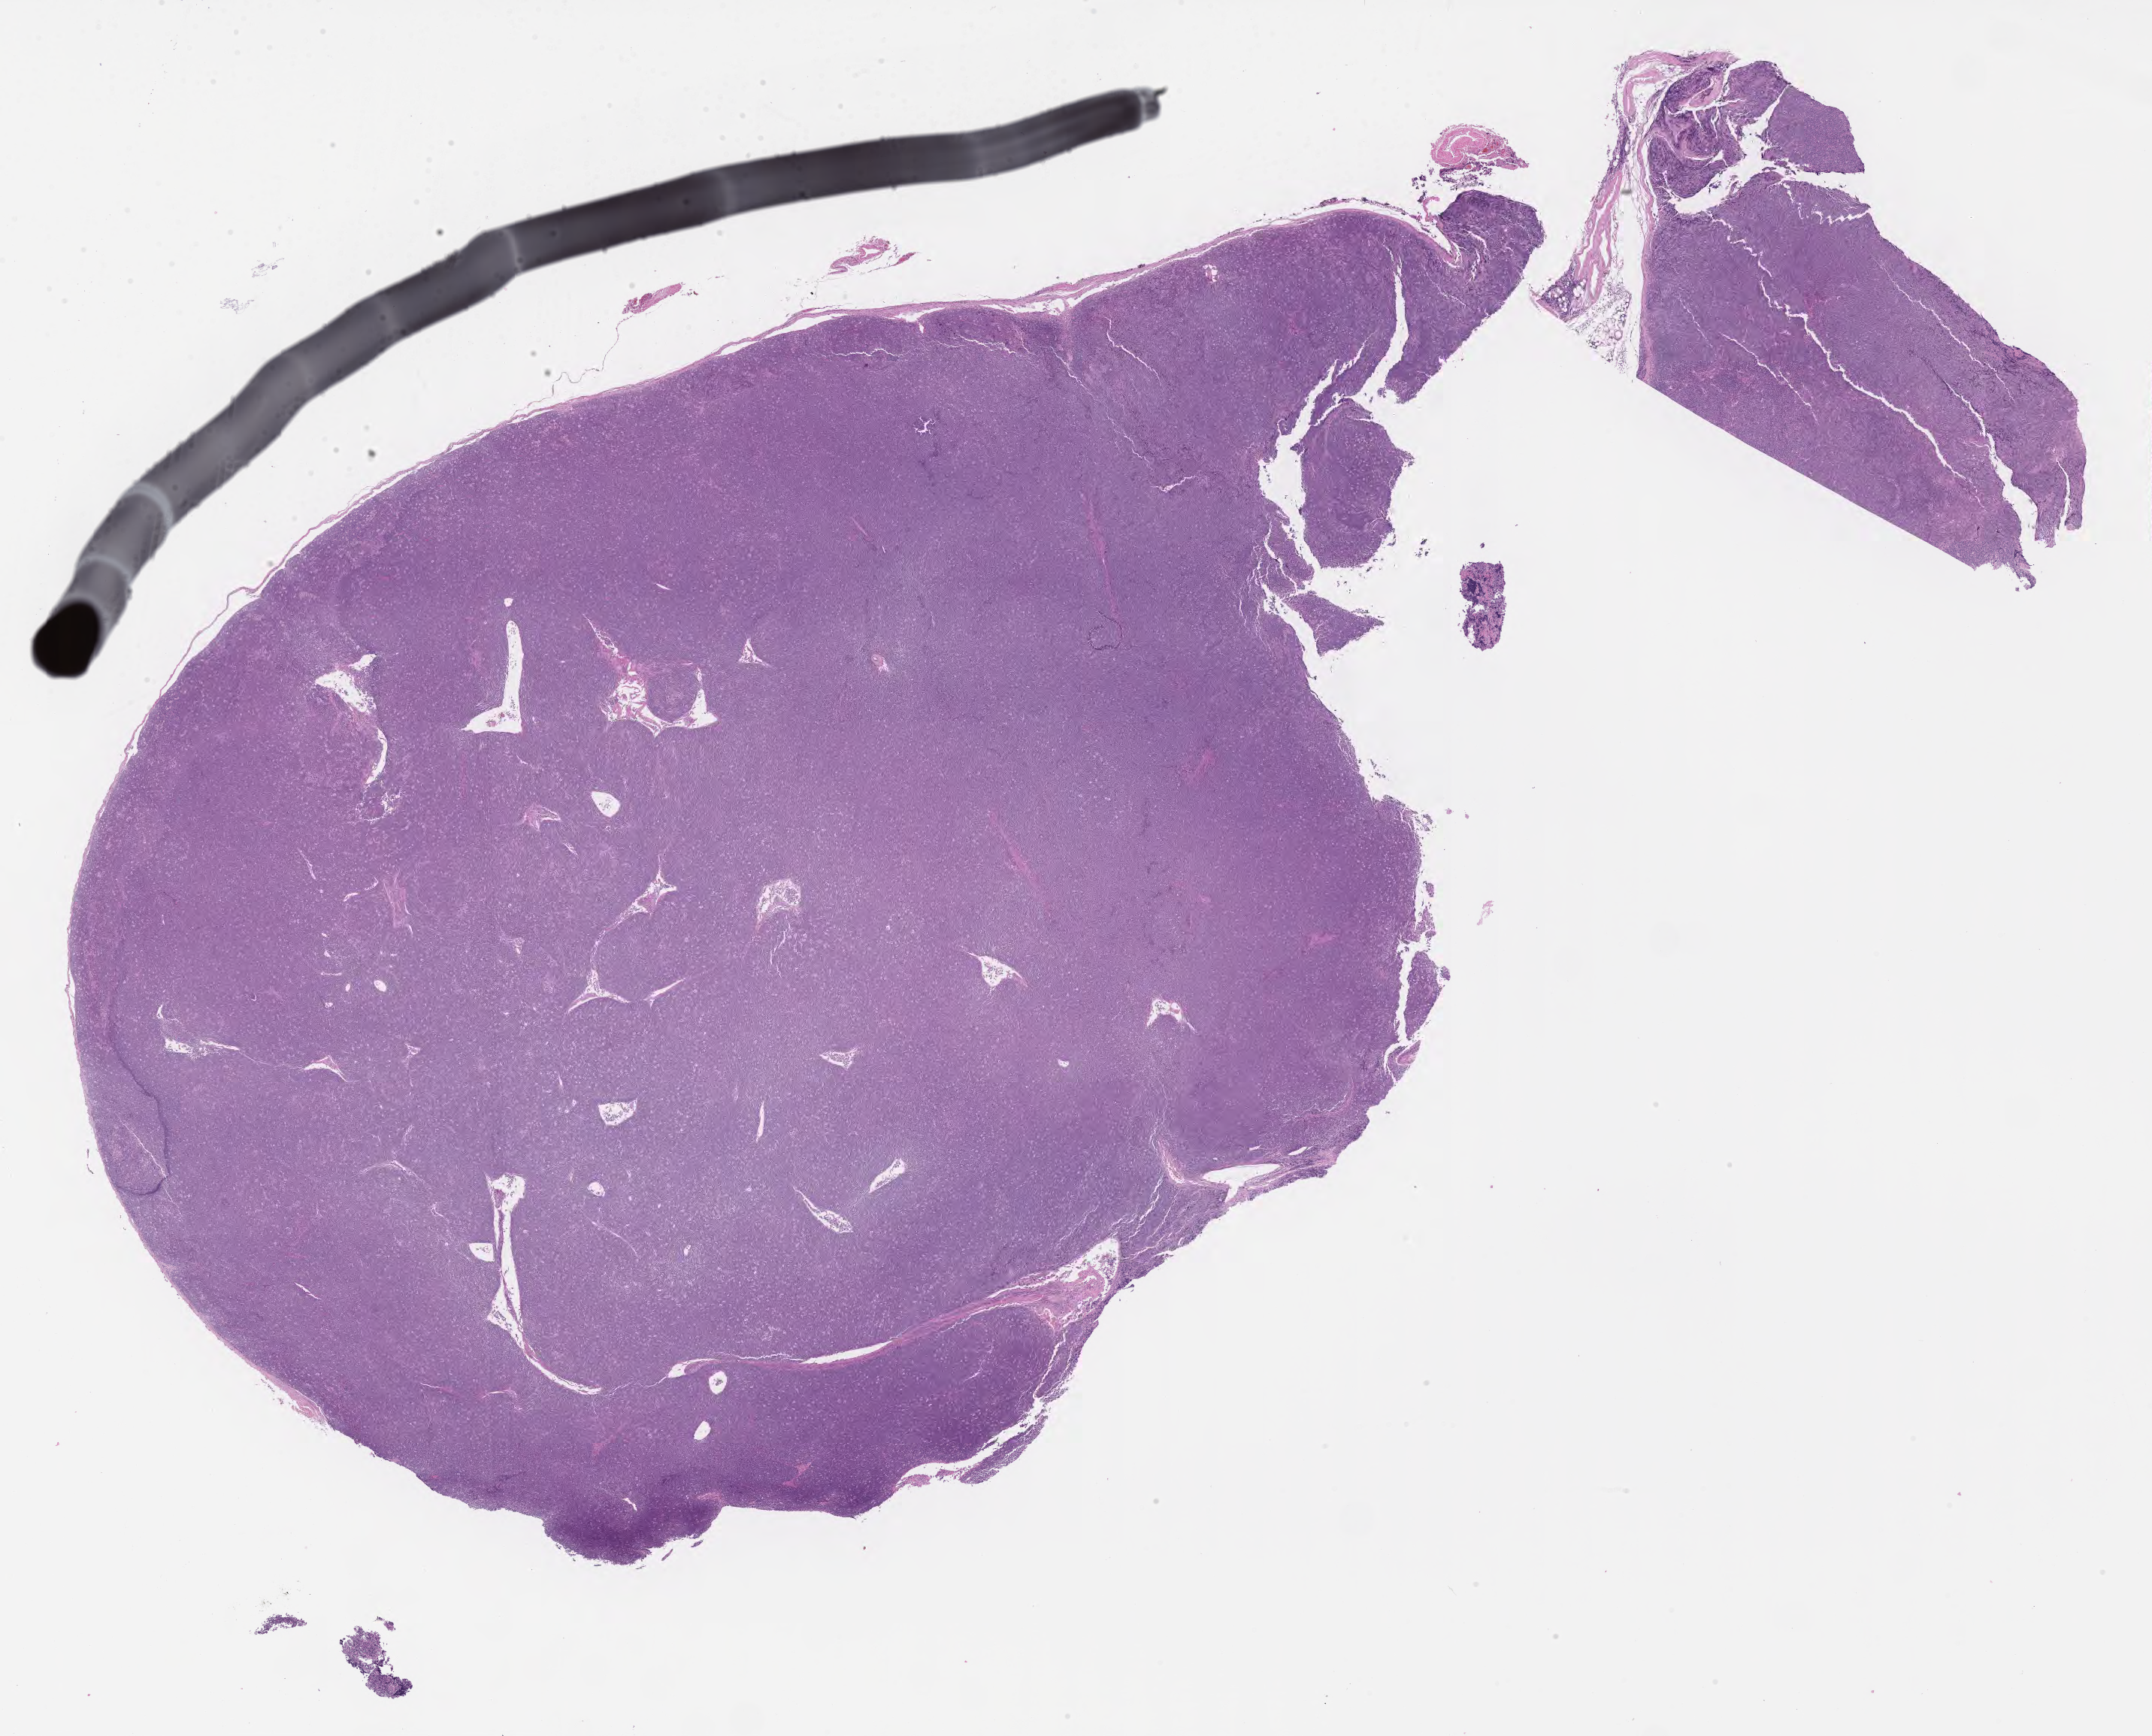
Digitized haematoxylin and eosin-stained section, shown as a low-resolution overview of the whole scanned area (about 23.1 x 18.7 mm), tumor tissue. Male patient; age at initial diagnosis 9 years.
Diagnosis: Burkitt lymphoma, NOS.